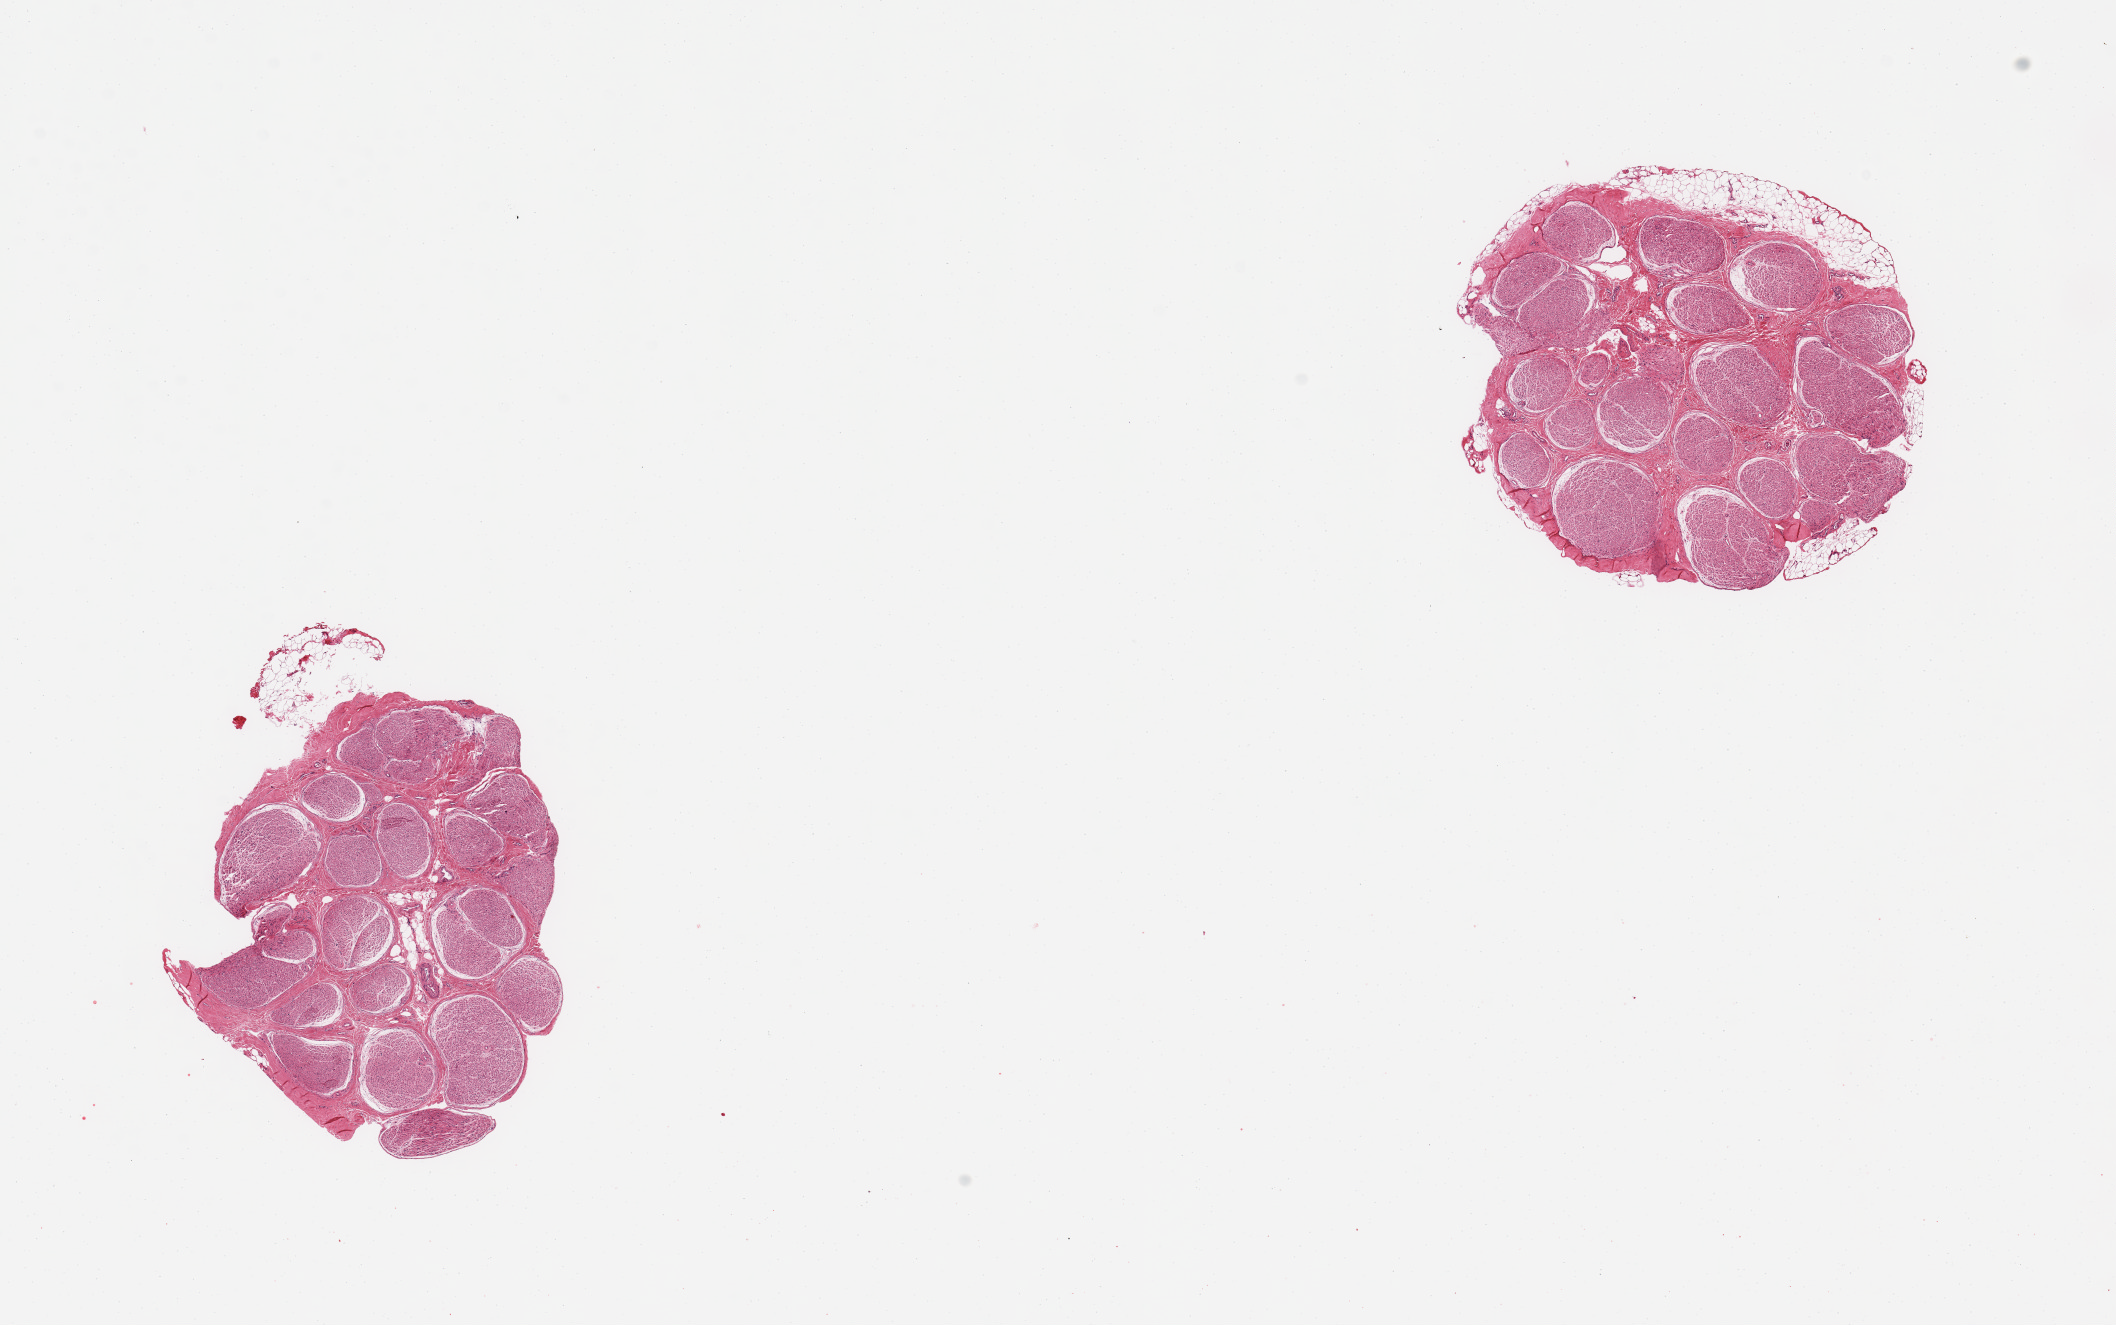
Whole-slide image, haematoxylin and eosin stain, brightfield — a low-resolution overview of the entire scanned area, about 16.7 x 10.5 mm. PAXgene-fixed, paraffin-embedded tissue. Section of tibial nerve (target tissue). Donor tissue sample. Donor sex: female.
Review note (as recorded): 2 pieces; foci of external fat up to 0.3 mm thick.